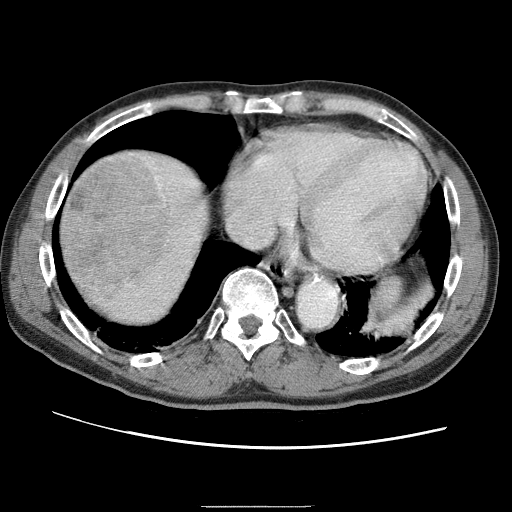
Contrast-enhanced abdominal CT (liver protocol), one axial slice; slice 63 of 75 in the series (ordered by position); reconstruction kernel STANDARD; 120 kVp; one of 2 acquisitions stored at this slice position; soft-tissue window (W 400 / L 40 HU); 2.5 mm slice thickness; 512 × 512 image matrix, field of view 360 × 360 mm. Case-level facts recorded for this patient, not image findings: diagnosis: hepatocellular carcinoma (patient treated with transarterial chemoembolisation; whether this scan precedes or follows treatment is not stated here); TNM stage (as recorded): Stage-II; Child-Pugh class: A; tumour differentiation: well differentiated; tumour size: 2 cm.
Structures marked on this image (semi-automatic segmentation, software-assisted and operator-edited):
- liver parenchyma outside the tumour (the mass and vessels are separate outlines, so this box may not span the whole liver): bounding box <58,146,214,328> (left, top, right, bottom; pixels)
- mass: <61,151,176,294>
- liver vessels: <190,261,193,264>